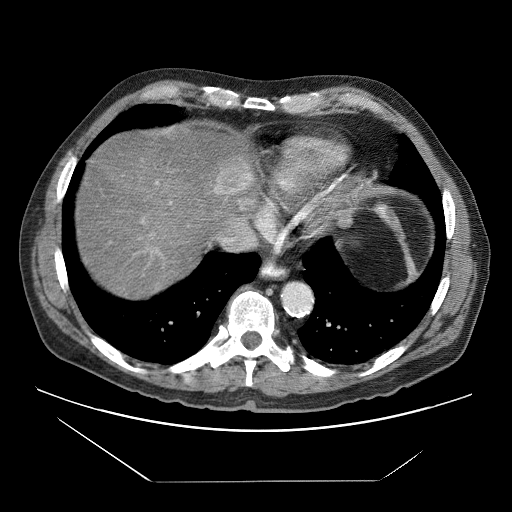
Contrast-enhanced abdominal CT (liver protocol), one axial slice. Position 66 of 83 along the scan axis. Reconstruction kernel STANDARD. 120 kVp. Soft-tissue window (W 400 / L 40 HU). 2.5 mm slice thickness. 512 × 512 image matrix, field of view 420 × 420 mm. From the clinical record (not read from this slice): diagnosis: hepatocellular carcinoma (patient treated with transarterial chemoembolisation; whether this scan precedes or follows treatment is not stated here); TNM stage (as recorded): Stage-IVB; Child-Pugh class: B; tumour differentiation: poorly differentiated.
Outlined on this slice (semi-automatic segmentation, software-assisted and operator-edited):
- liver parenchyma outside the tumour (the mass and vessels are separate outlines, so this box may not span the whole liver): bounding box (x1, y1, x2, y2) in pixels: (76, 124, 254, 297)
- mass: (213, 154, 261, 210)
- liver vessels: (142, 181, 172, 253)